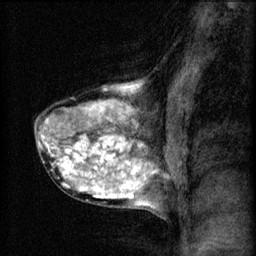
Breast MRI (dynamic contrast-enhanced), one sagittal slice. Slice 37 of 60 in the series (ordered by position). 3 images stored at this slice position (order not interpretable as contrast timing). 1.5 T. TE 4.2 ms, TR 8.2 ms. 256 × 256 image matrix, field of view 180 × 180 mm. Female patient, age 40 years.
Outlined on this slice (semi-automatic segmentation, software-assisted and operator-edited):
- analysis volume of interest (the breast-tissue region the enhancement analysis was run in; not a lesion): bounding box (x1, y1, x2, y2) in pixels: (34, 80, 167, 211)
- tumour enhancement mask (voxels above the 70 % enhancement threshold inside the analysis volume of interest): (42, 84, 155, 207)